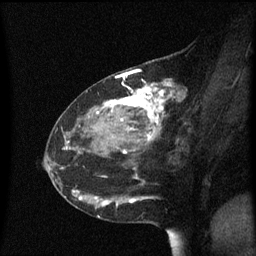
Breast MRI (dynamic contrast-enhanced), one sagittal slice. Position 28 of 60 along the scan axis. Dynamic contrast-enhanced series, image 2 of 3 at this slice position (ordered by acquisition). 1.5 T. TE 4.2 ms, TR 8.4 ms. 256 × 256 image matrix, field of view 200 × 200 mm. Patient: female, 48 years. Case-level facts recorded for this patient, not image findings: setting: breast cancer imaged before/during neoadjuvant chemotherapy; receptor status: HR-positive, HER2-negative.
Outlined on this slice (semi-automatically segmented with operator editing):
- analysis volume of interest (the breast-tissue region the enhancement analysis was run in; not a lesion): bounding box [x1, y1, x2, y2] px = [80, 78, 191, 221]
- tumour enhancement mask (voxels above the 70 % enhancement threshold inside the analysis volume of interest): [96, 82, 185, 203]